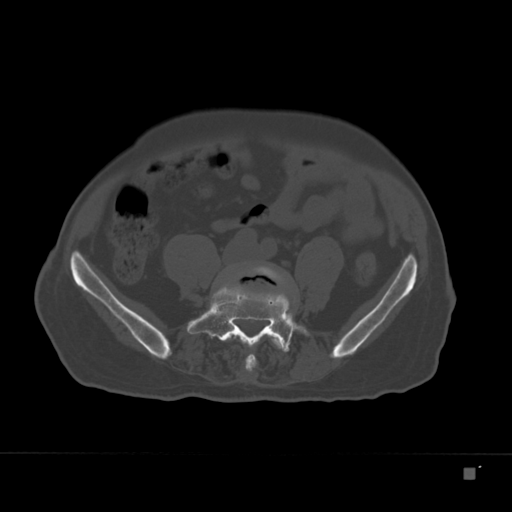
CT including the spine, one axial slice. Position 29 of 332 along the scan axis. Reconstruction kernel Br40s. 120 kVp. Bone window (W 1800 / L 400 HU). 1.5 mm slice thickness. 512 × 512 image matrix. Male patient, age 72 years. Case-level facts recorded for this patient, not image findings: primary cancer: skeletal.
Outlined on this slice (semi-automatically segmented with operator editing):
- L4 vertebra: box from (x=245, y=265) to (x=287, y=372) px
- L5 vertebra: (x=192, y=282)–(x=307, y=350)